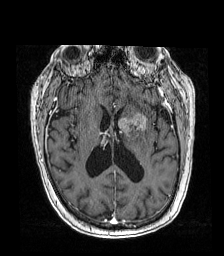
Brain MRI from a brain-tumour surgery series, one axial slice; position 79 of 192 along the scan axis; T1-weighted post-contrast; 1 mm slice thickness; 224 × 256 image matrix, field of view 219 × 250 mm. Case-level facts recorded for this patient, not image findings: histopathology: Metastatic carcinoma from lung primary.
Outlined on this slice (expert manual segmentation):
- tumour: box from (x=117, y=111) to (x=148, y=137) px